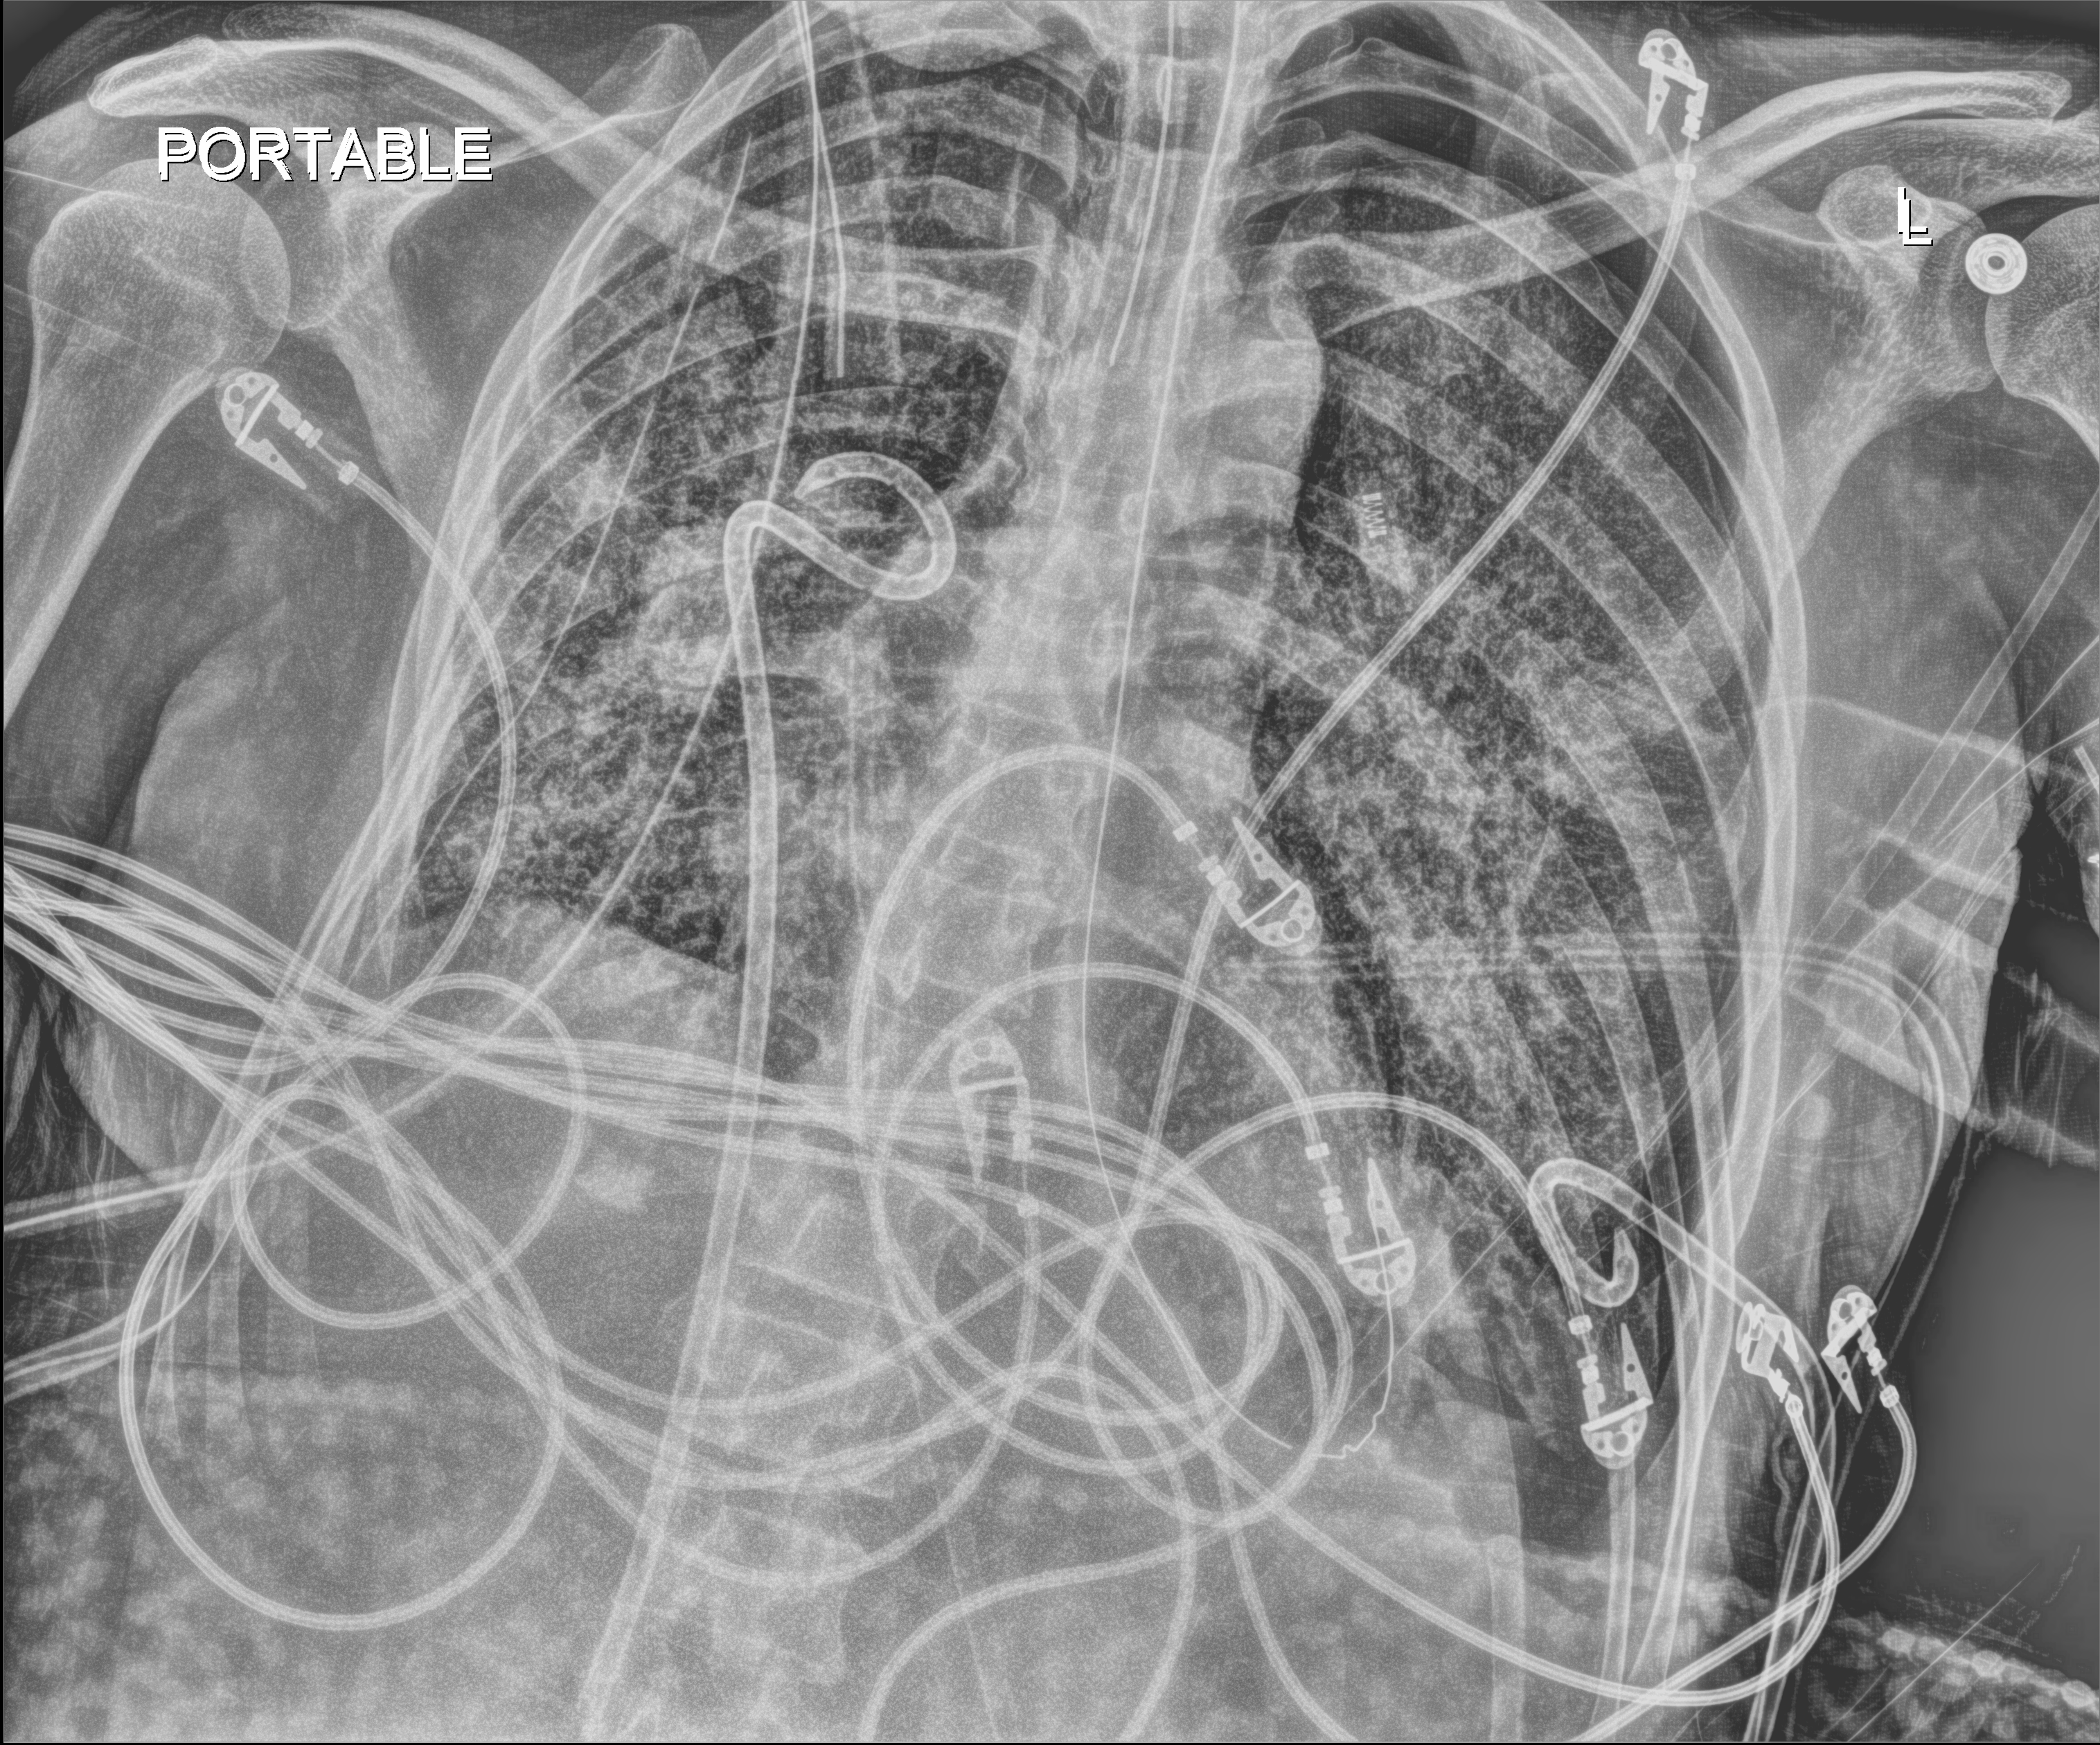
Chest X-ray, anteroposterior (AP) projection. Adult patient hospitalised with COVID-19, age 18–59 years.
Hospital-stay facts (about this admission, not read from this image; timing relative to this image not recorded): hypertension (admission record): no; chronic kidney disease (admission record): no; length of hospital stay: 41 days.